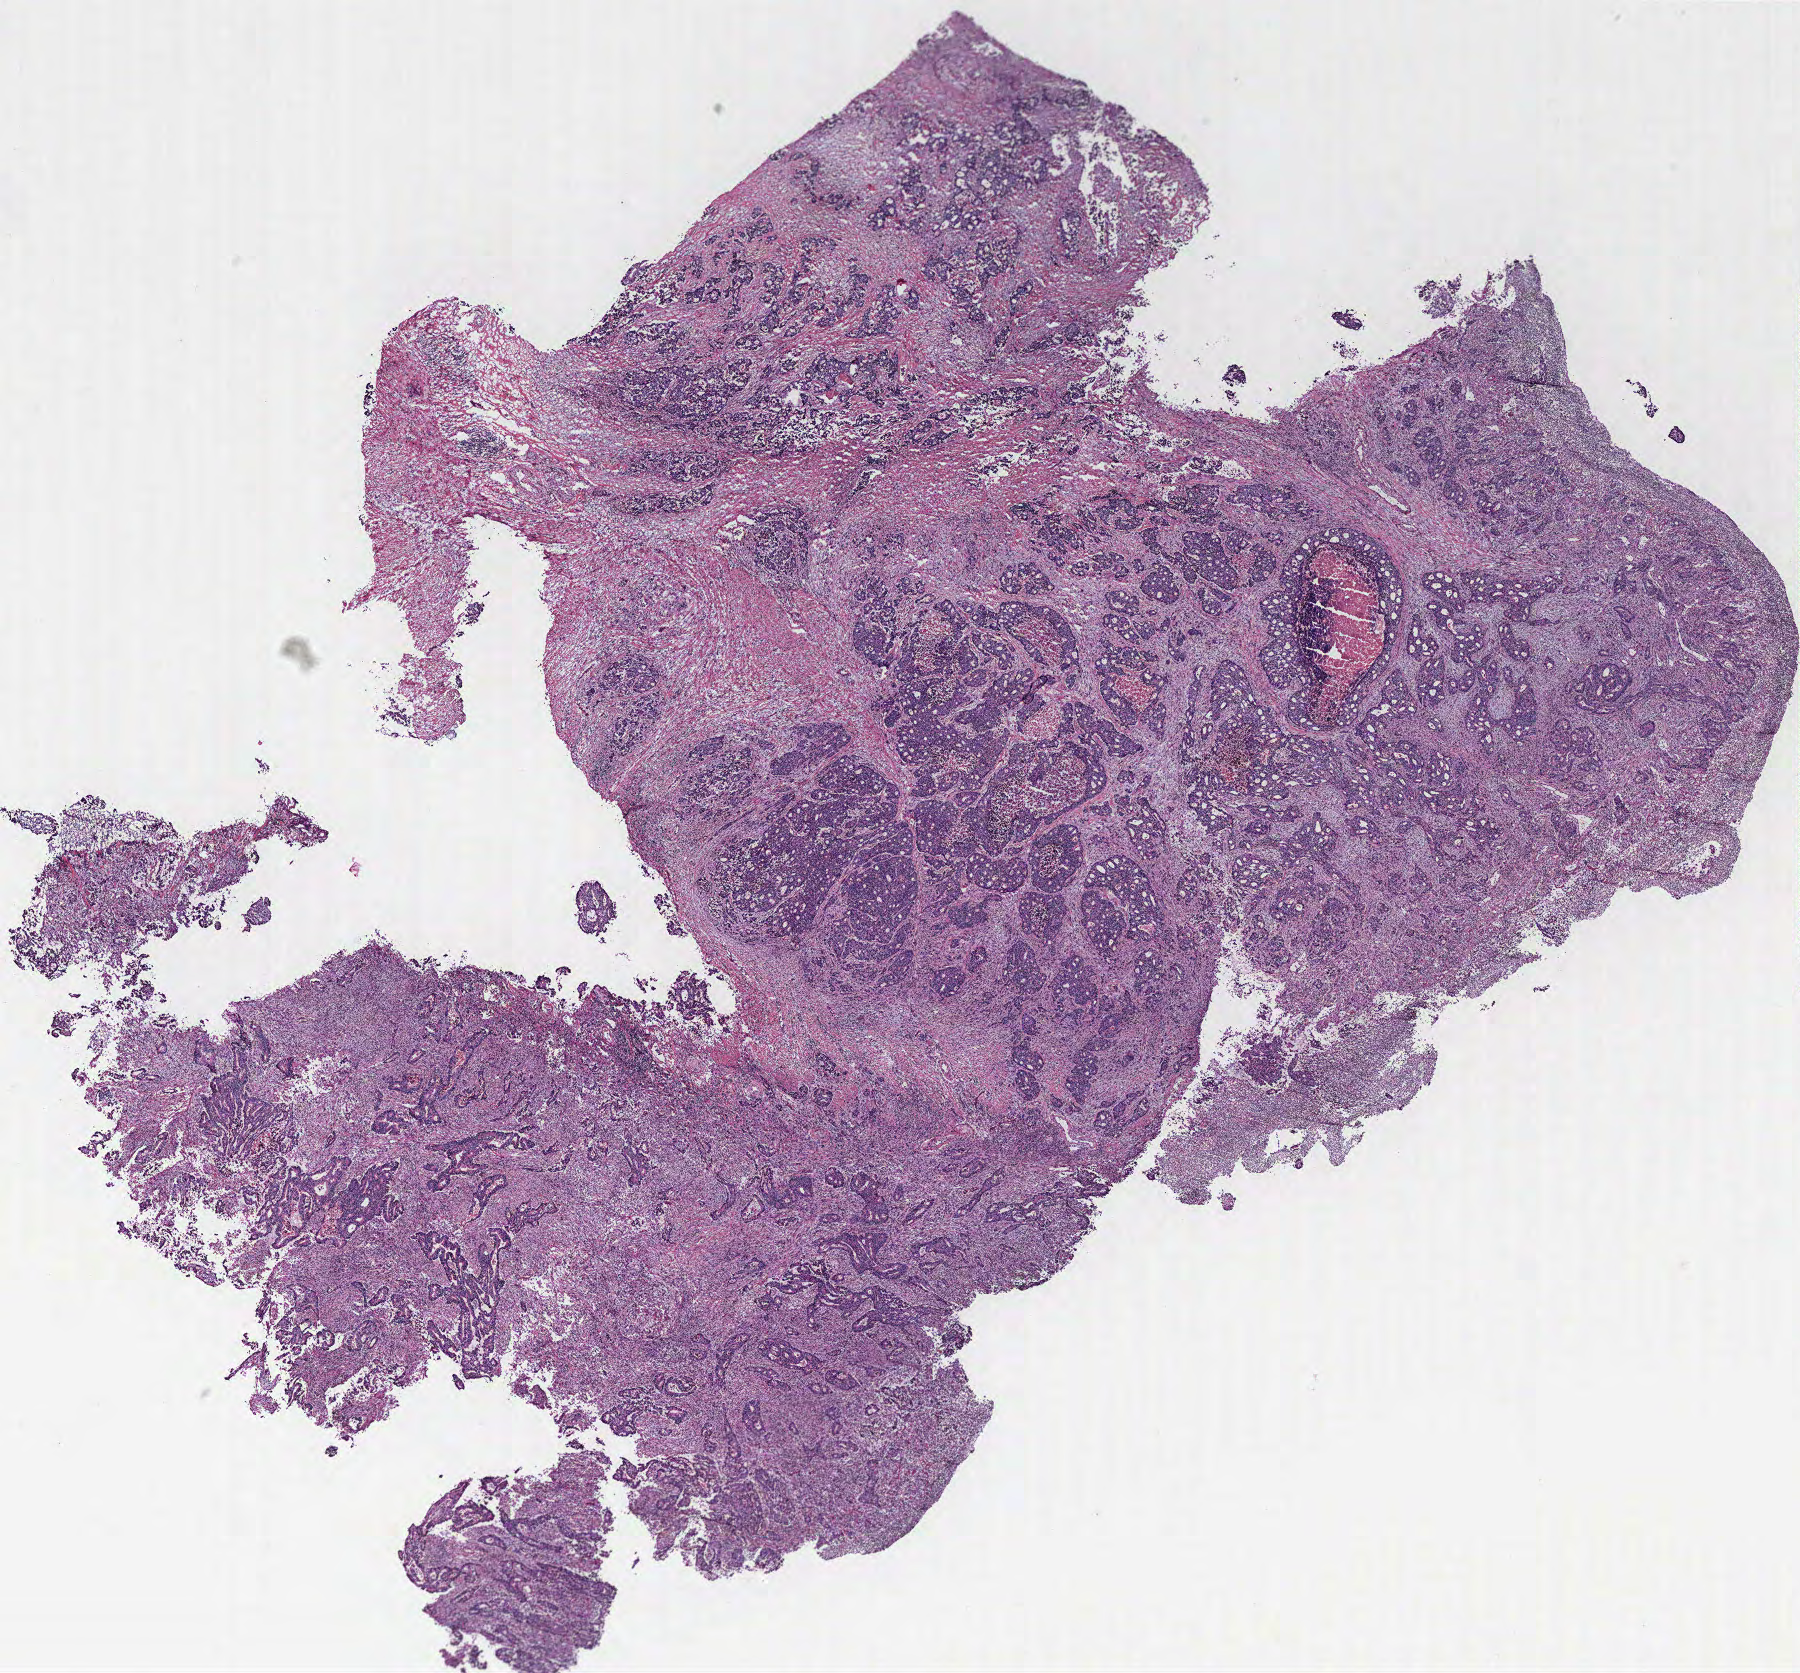
H&E-stained whole-slide image, whole scanned area (about 14.4 x 13.4 mm) shown as a low-resolution overview, colon, tumour tissue. Male, 64 y/o.
Primary tumour site (as recorded): colon. AJCC pathologic stage: IVA. Diagnosis: Adenocarcinoma, NOS.